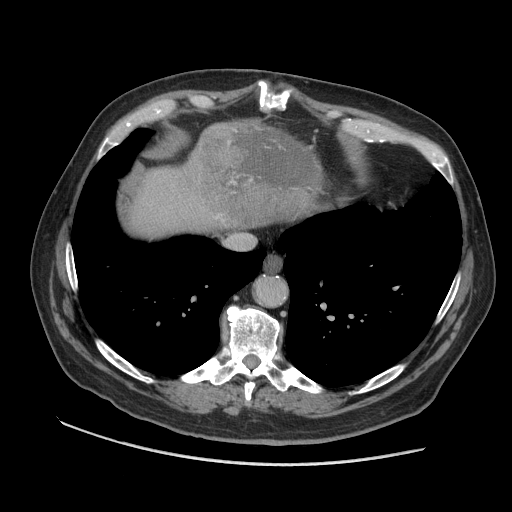
Contrast-enhanced abdominal CT (liver protocol), one axial slice; position 91 of 109 along the scan axis; 140 kVp; soft-tissue window (W 400 / L 40 HU); 2.5 mm slice thickness; 512 × 512 image matrix, field of view 420 × 420 mm. From the clinical record (not read from this slice): diagnosis: hepatocellular carcinoma (patient treated with transarterial chemoembolisation; whether this scan precedes or follows treatment is not stated here); TNM stage (as recorded): Stage-I; Child-Pugh class: A.
Structures marked on this image (semi-automatic segmentation, software-assisted and operator-edited):
- liver parenchyma outside the tumour (the mass and vessels are separate outlines, so this box may not span the whole liver): box from (x=129, y=145) to (x=263, y=236) px
- mass: (x=190, y=119)–(x=327, y=227)